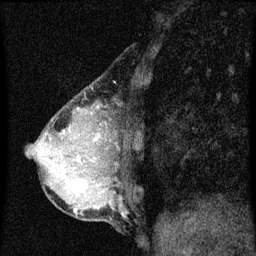
Breast MRI (dynamic contrast-enhanced), one sagittal slice; position 18 of 60 along the scan axis; dynamic contrast-enhanced series, image 2 of 3 at this slice position (ordered by acquisition); 1.5 T; TE 4.2 ms, TR 8 ms; 2 mm slice thickness; 256 × 256 image matrix. Patient: female, 49 years.
Annotated regions visible in this slice (semi-automatic segmentation, software-assisted and operator-edited):
- analysis volume of interest (the breast-tissue region the enhancement analysis was run in; not a lesion): bounding box (x1, y1, x2, y2) in pixels: (44, 174, 89, 201)
- tumour enhancement mask (voxels above the 70 % enhancement threshold inside the analysis volume of interest): (71, 182, 84, 193)